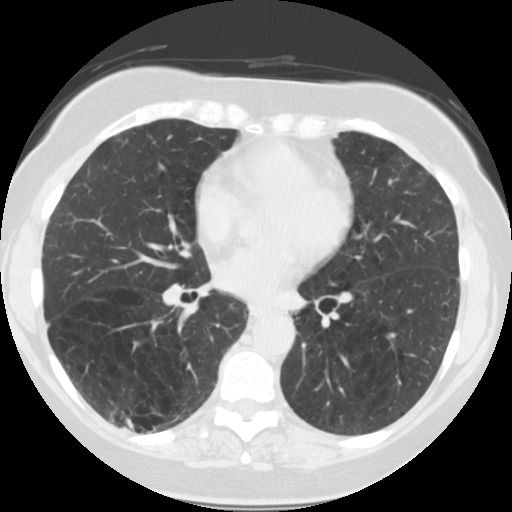
Axial slice from a low-dose chest CT screening exam; first (baseline) screen; lung window (W 1500 / L -600 HU); 2.5 mm slice thickness; slice 72 of 121 in the series; 512 × 512 image matrix, field of view 309 × 309 mm. Female participant, aged 59 years at enrolment. Current smoker at enrolment.
- Lesion marked by an expert reader, bounding box (x1, y1, x2, y2) in pixels: (101, 400, 155, 448).
- Screening reader's record for this exam: no non-calcified nodule ≥4 mm recorded.
- Official screen result: negative screen, significant abnormalities not suspicious for lung cancer.